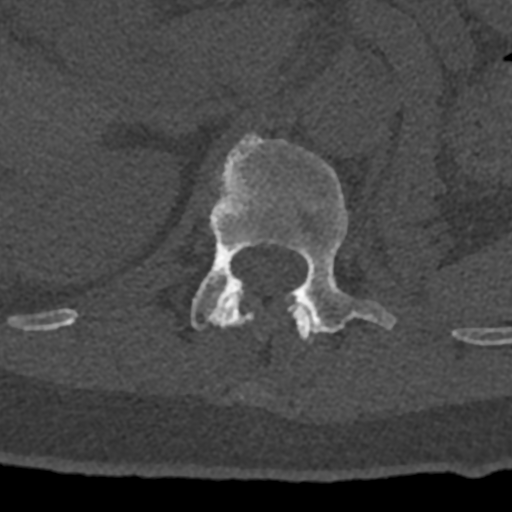
CT including the spine, one axial slice. Slice 453 of 797 in the series (ordered by position). Reconstruction kernel Br40s/3. Bone window (W 1800 / L 400 HU). 0.5 mm slice thickness. 512 × 512 image matrix, field of view 160 × 160 mm. Male patient, age 74 years. From the clinical record (not read from this slice): primary cancer: renal.
Structures marked on this image (semi-automatic segmentation, software-assisted and operator-edited):
- L1 vertebra: box from (x=191, y=133) to (x=396, y=333) px
- T12 vertebra: (x=70, y=298)–(x=315, y=341)